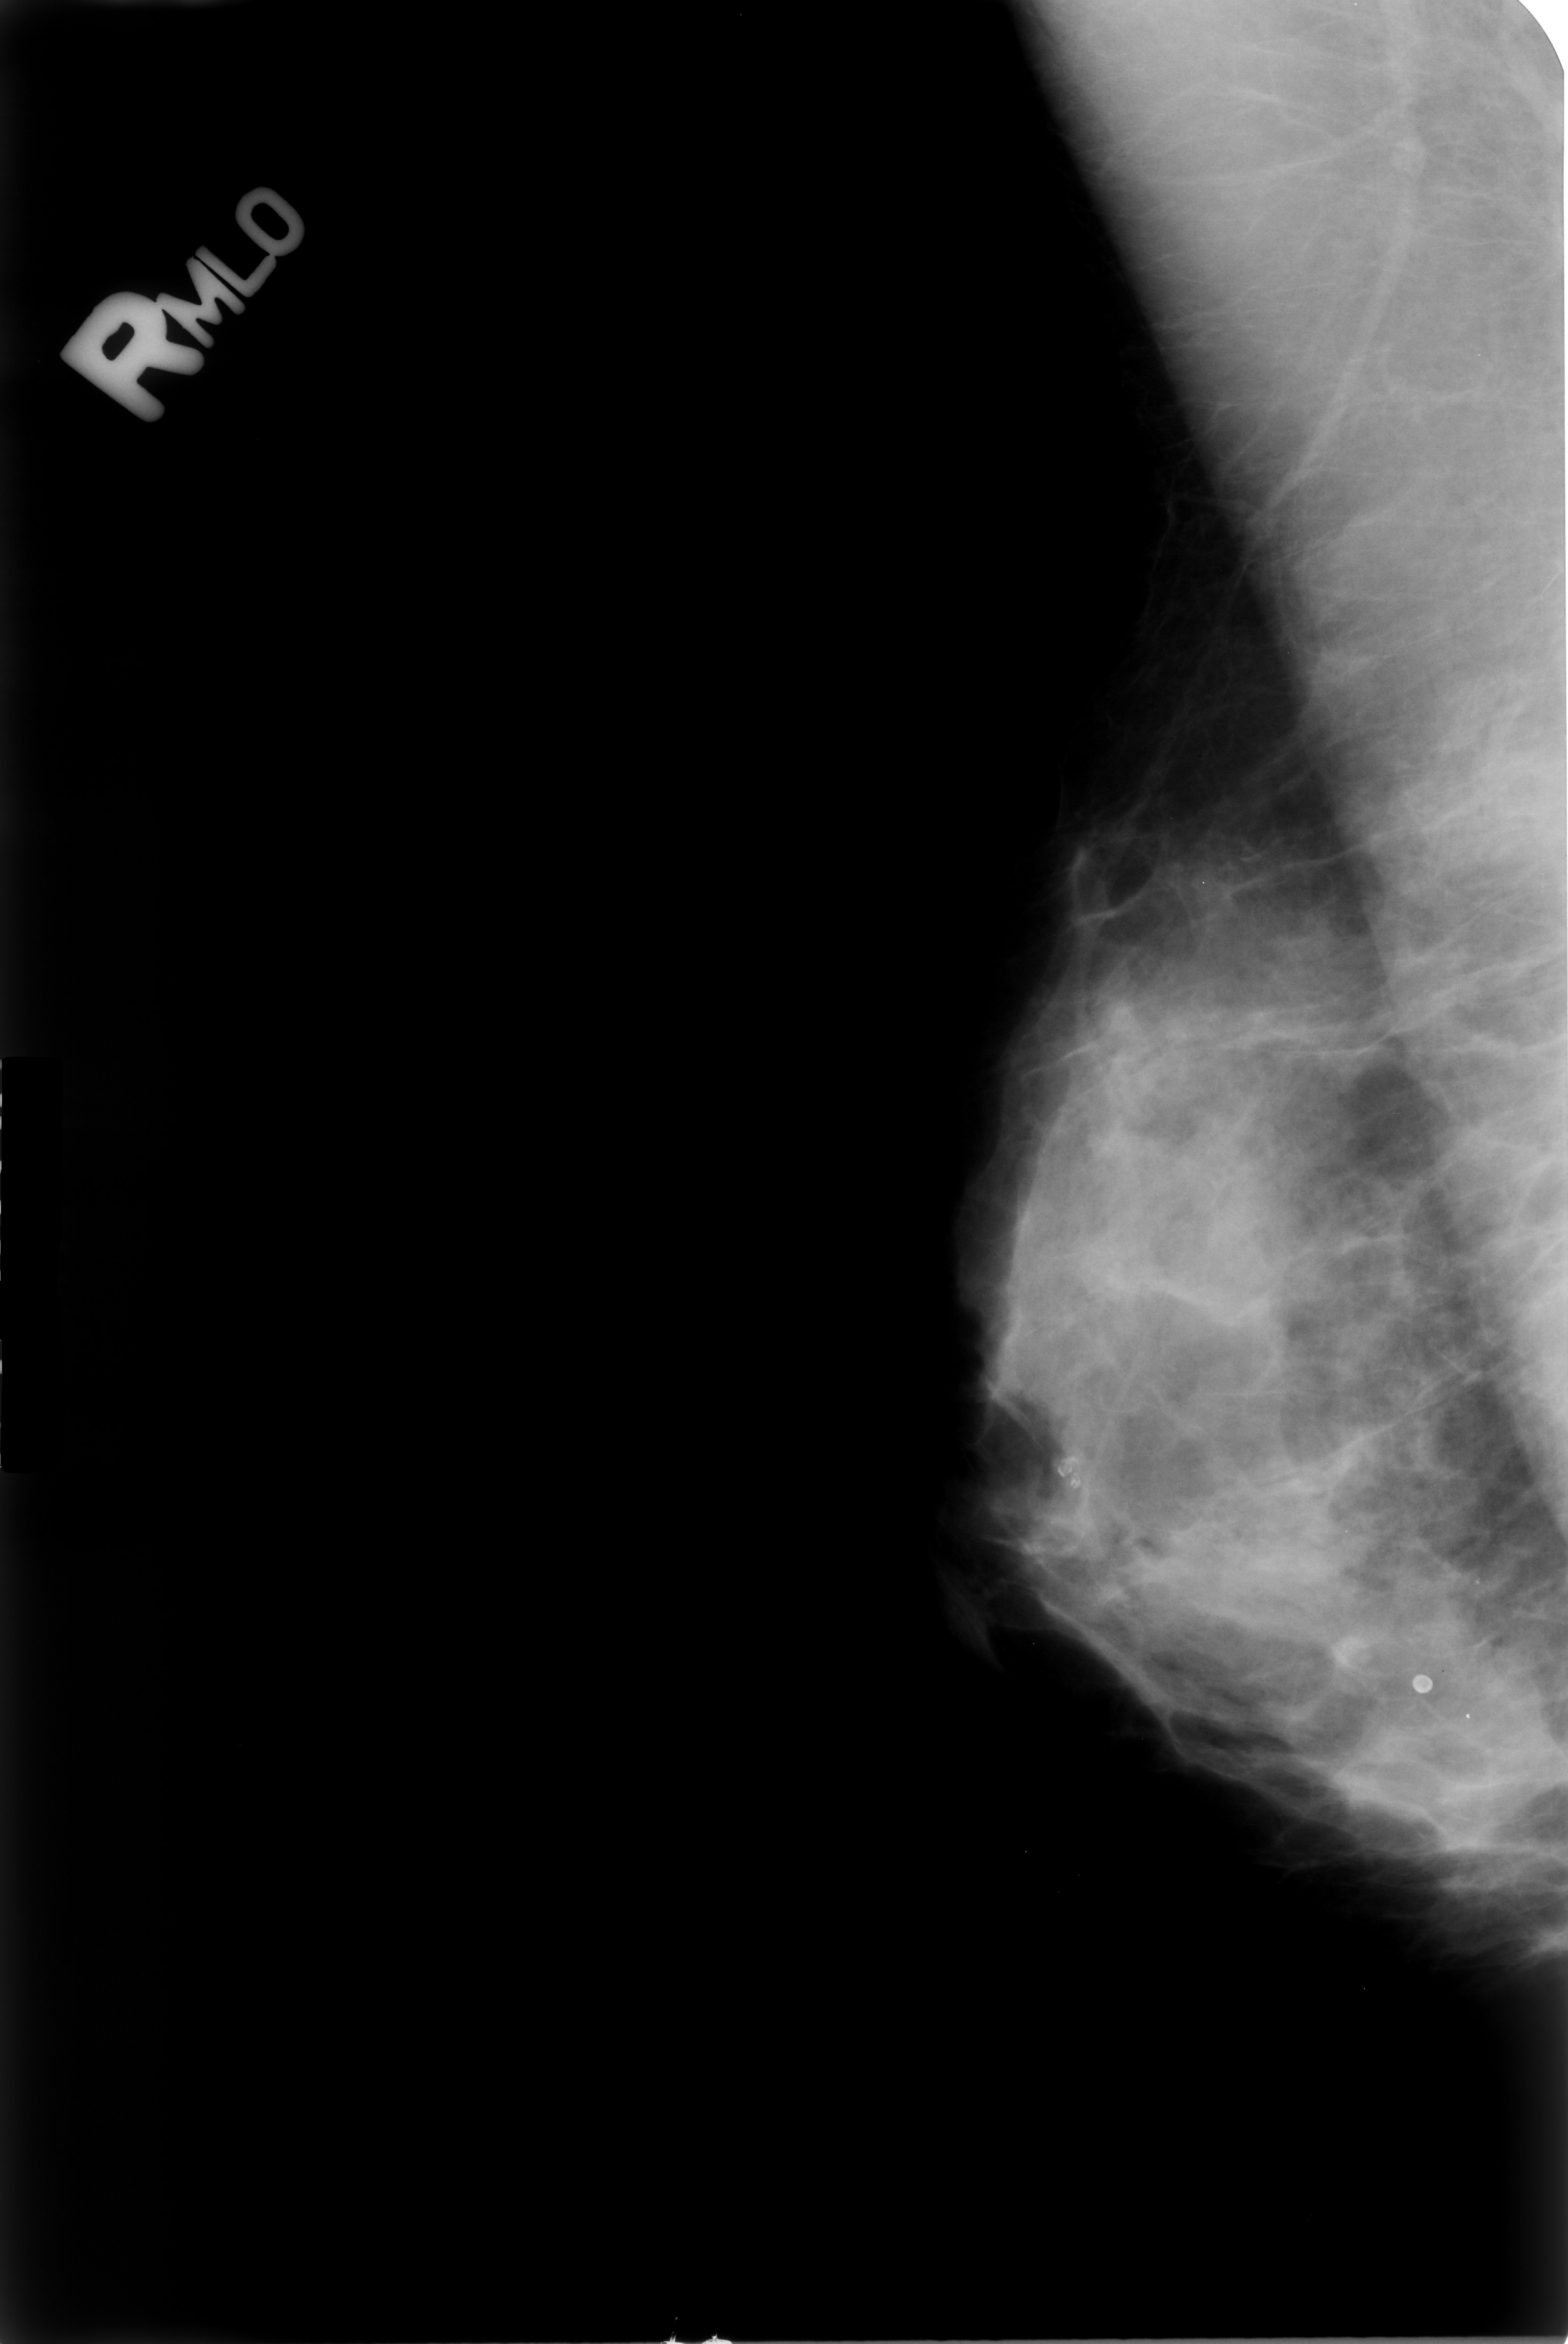
Mammogram (digitized film), right breast, mediolateral oblique (MLO) view.
Marked findings (only marked abnormalities are described; nothing is implied about the rest of the image): Finding 1 of 2: calcifications, morphology lucent center; BI-RADS assessment category 2; benign; no additional work-up was recommended (benign without callback). Finding 2 of 2: calcifications, morphology lucent center; BI-RADS assessment category 2; subtlety rating 5 on a 1 (subtle) to 5 (obvious) scale; benign without callback (not worked up further).